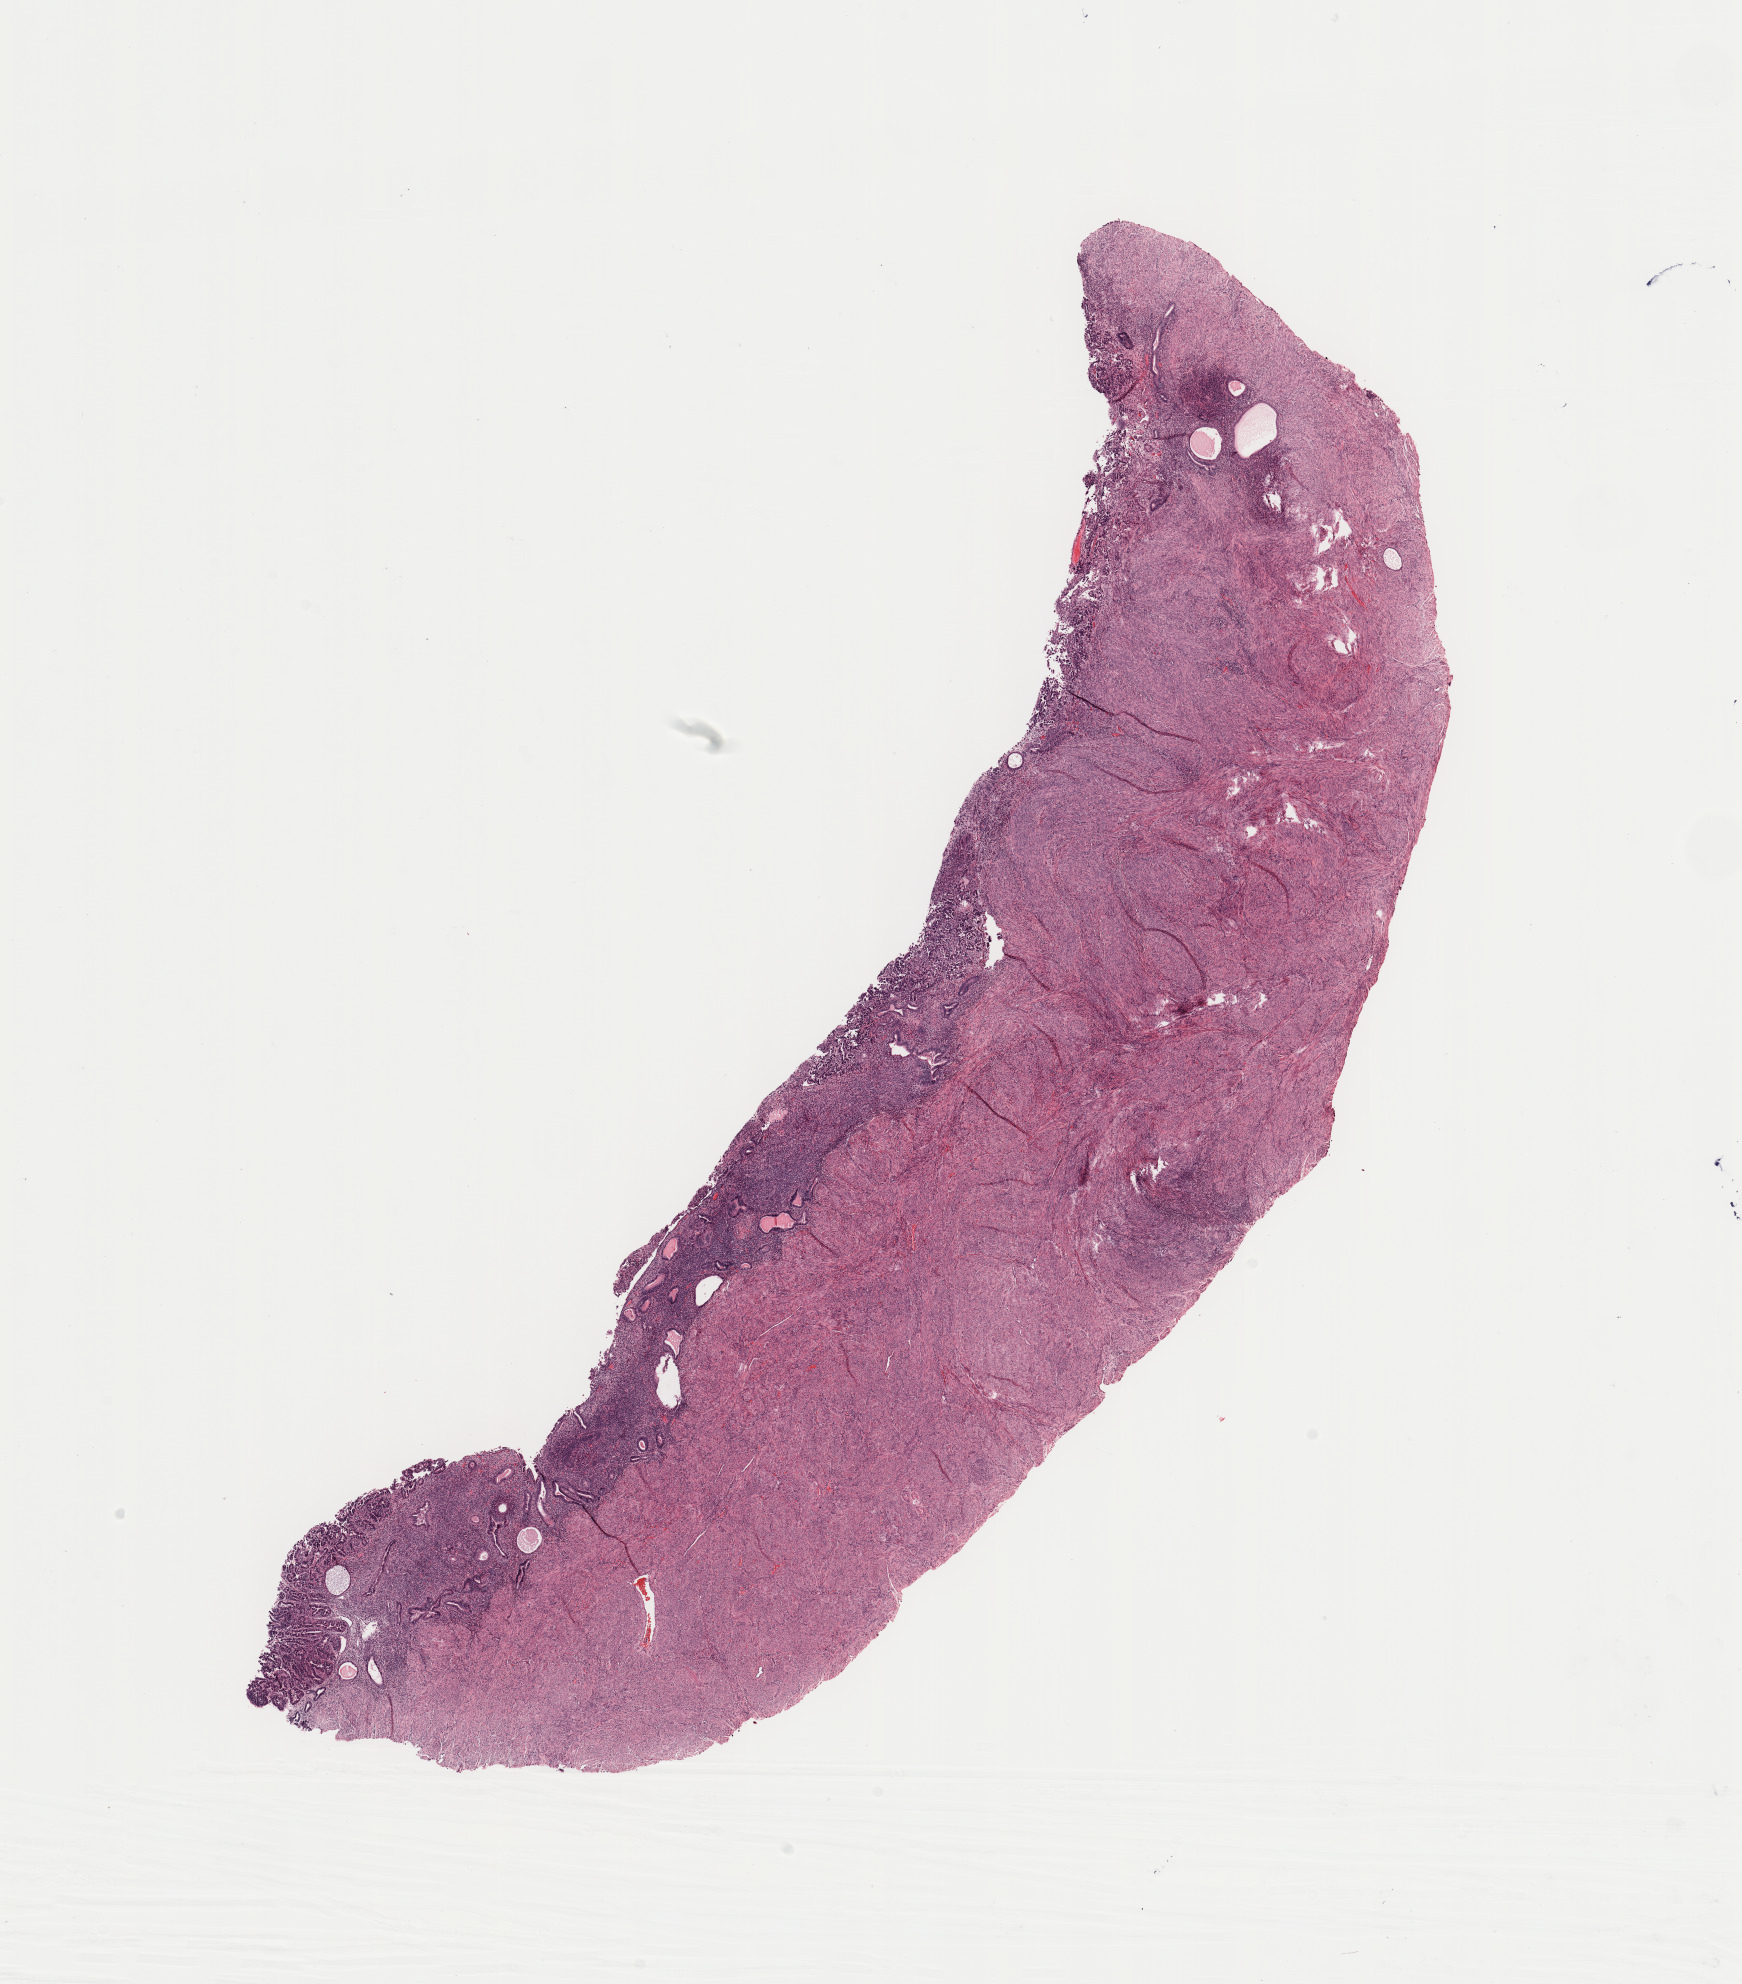
Whole-slide histology image, Hematoxylin and eosin (H&E) stained — a low-resolution overview of the entire scanned area, about 13.8 x 15.7 mm (from a 20x scan), uterus, normal (non-tumour) tissue. 69-year-old female patient.
This section: normal (non-tumour) tissue from the same patient. Patient diagnosis (cohort enrolment): corpus endometrial carcinoma (uterus).